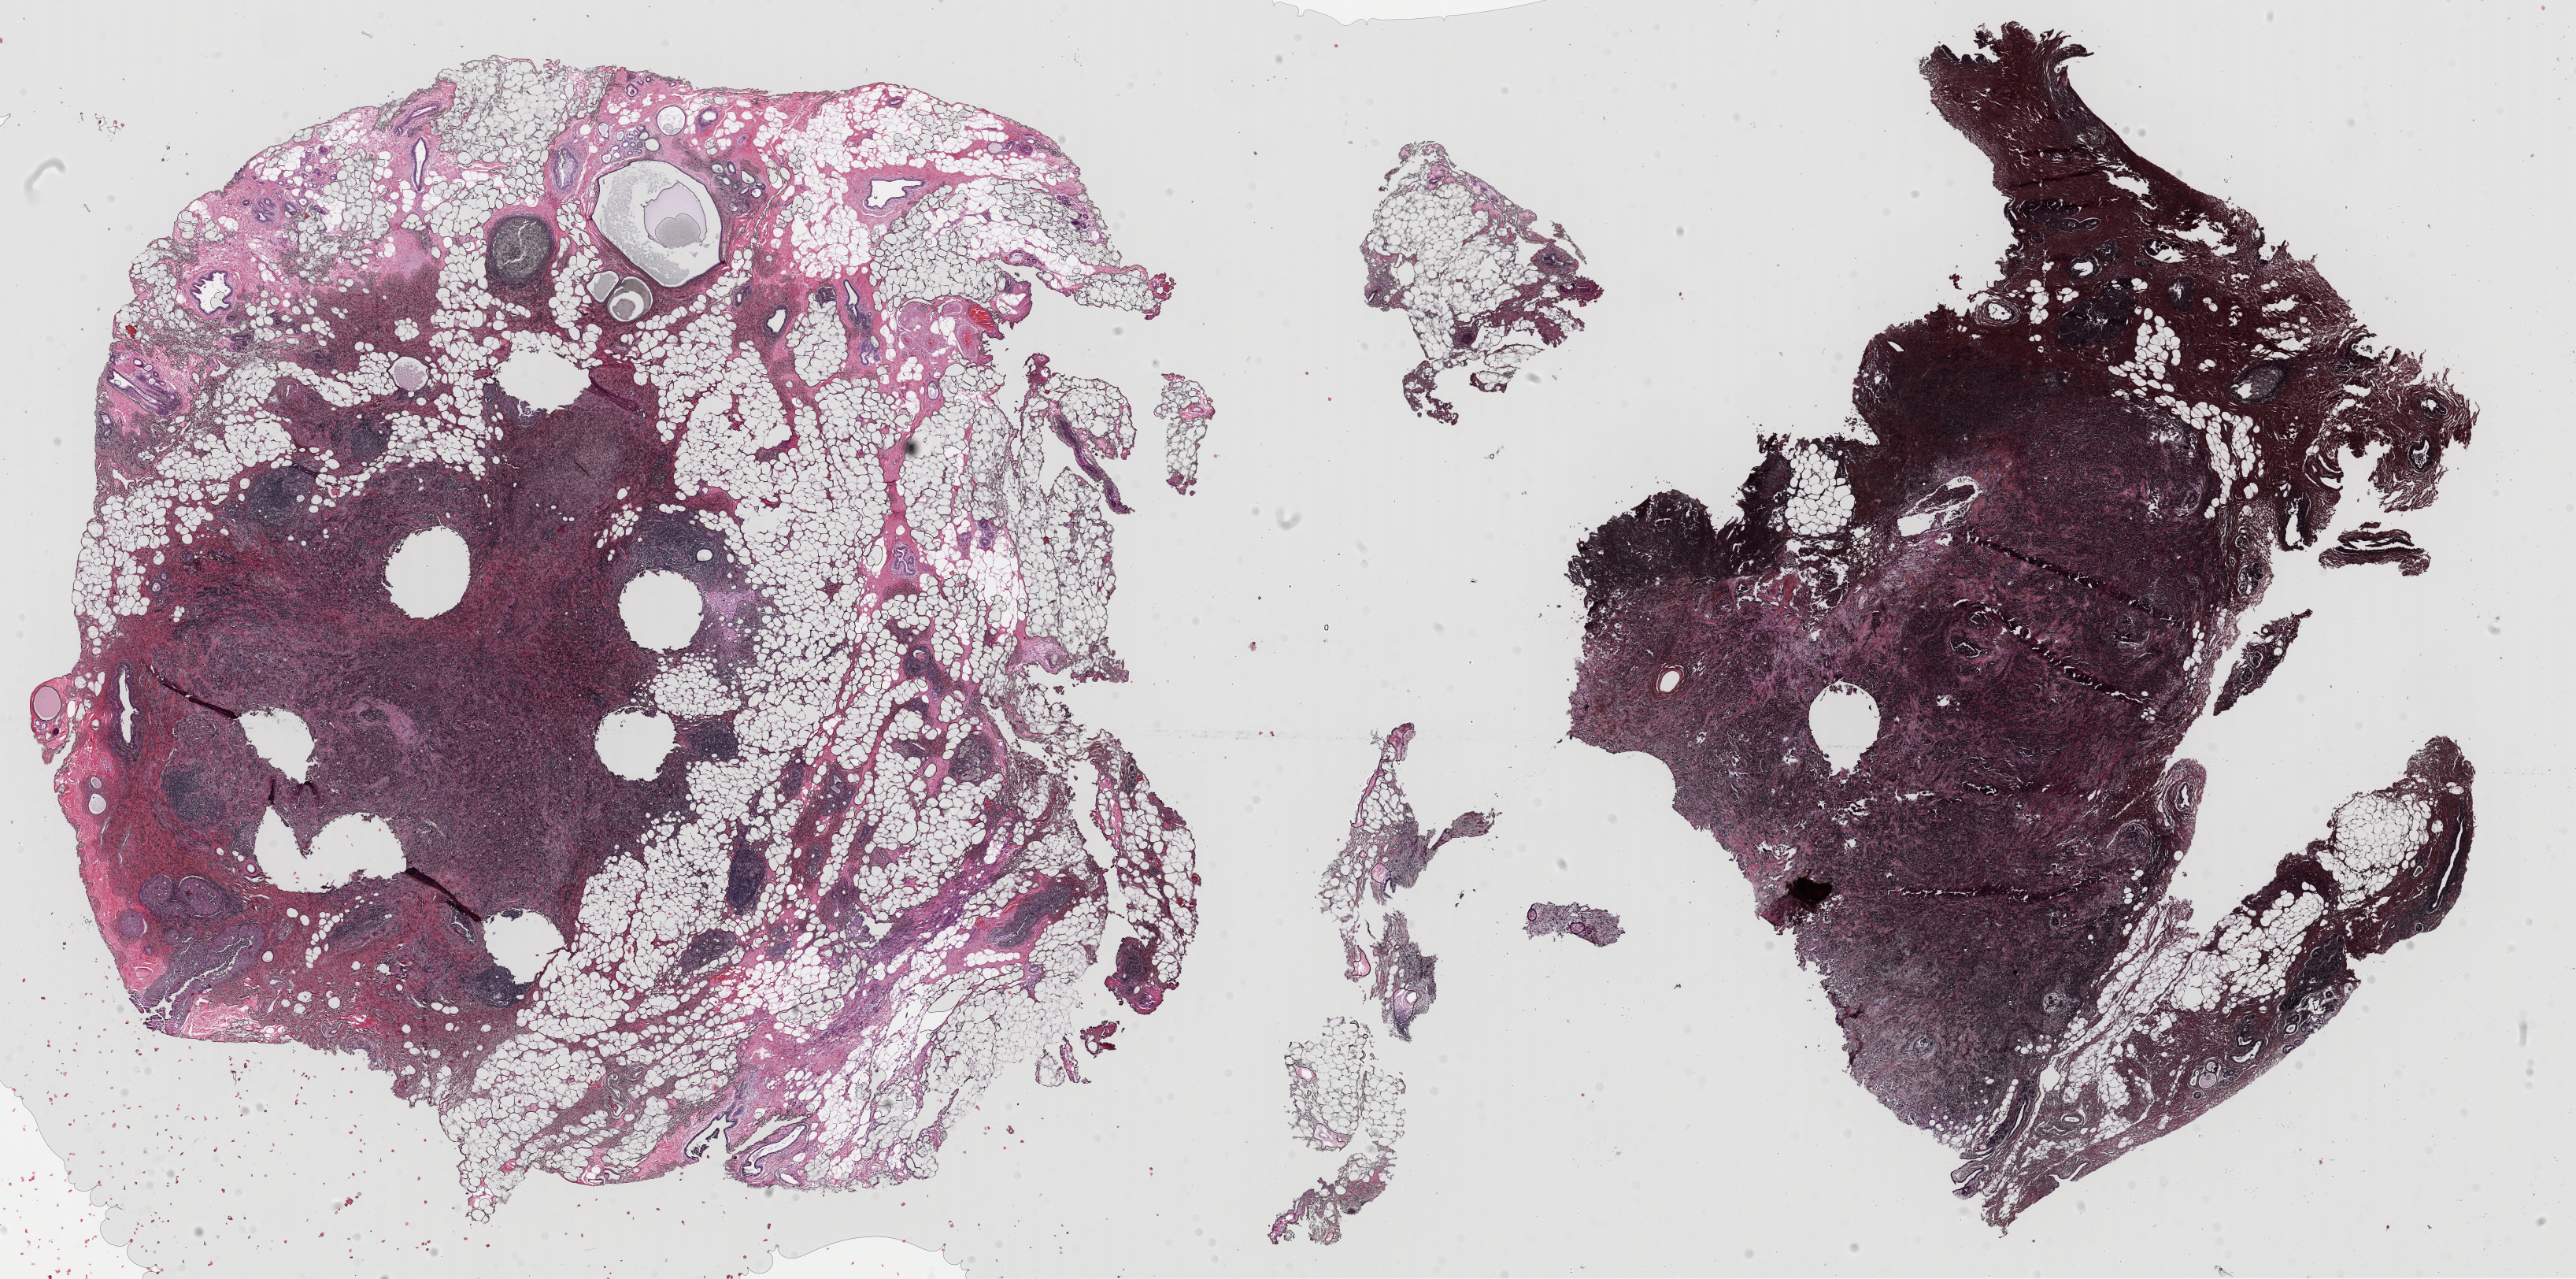
H&E whole-slide image — a low-resolution overview of the entire scanned area, about 25.8 x 12.8 mm (from a 40x scan). Formalin-fixed paraffin-embedded (FFPE) diagnostic section. Primary tumour sample from the breast. Female, age 80 years at initial diagnosis.
- pathologic diagnosis: Infiltrating duct carcinoma, NOS
- lymph nodes positive (case pathology): 0 of 1 examined
- AJCC pathologic stage: I (6th edition)